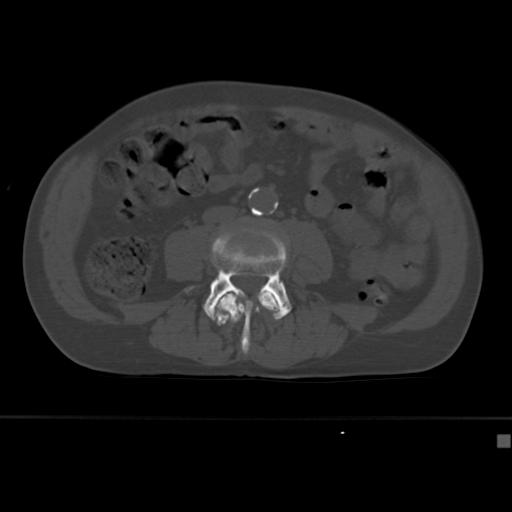
CT including the spine, one axial slice; position 113 of 430 along the scan axis; reconstruction kernel Br40s; 120 kVp; bone window (W 1800 / L 400 HU); 1.5 mm slice thickness; 512 × 512 image matrix. Male patient, age 64 years. From the clinical record (not read from this slice): primary cancer: uterus.
Outlined on this slice (semi-automatic segmentation, software-assisted and operator-edited):
- L3 vertebra: bounding box <215,292,280,346> (left, top, right, bottom; pixels)
- L4 vertebra: <185,228,292,354>